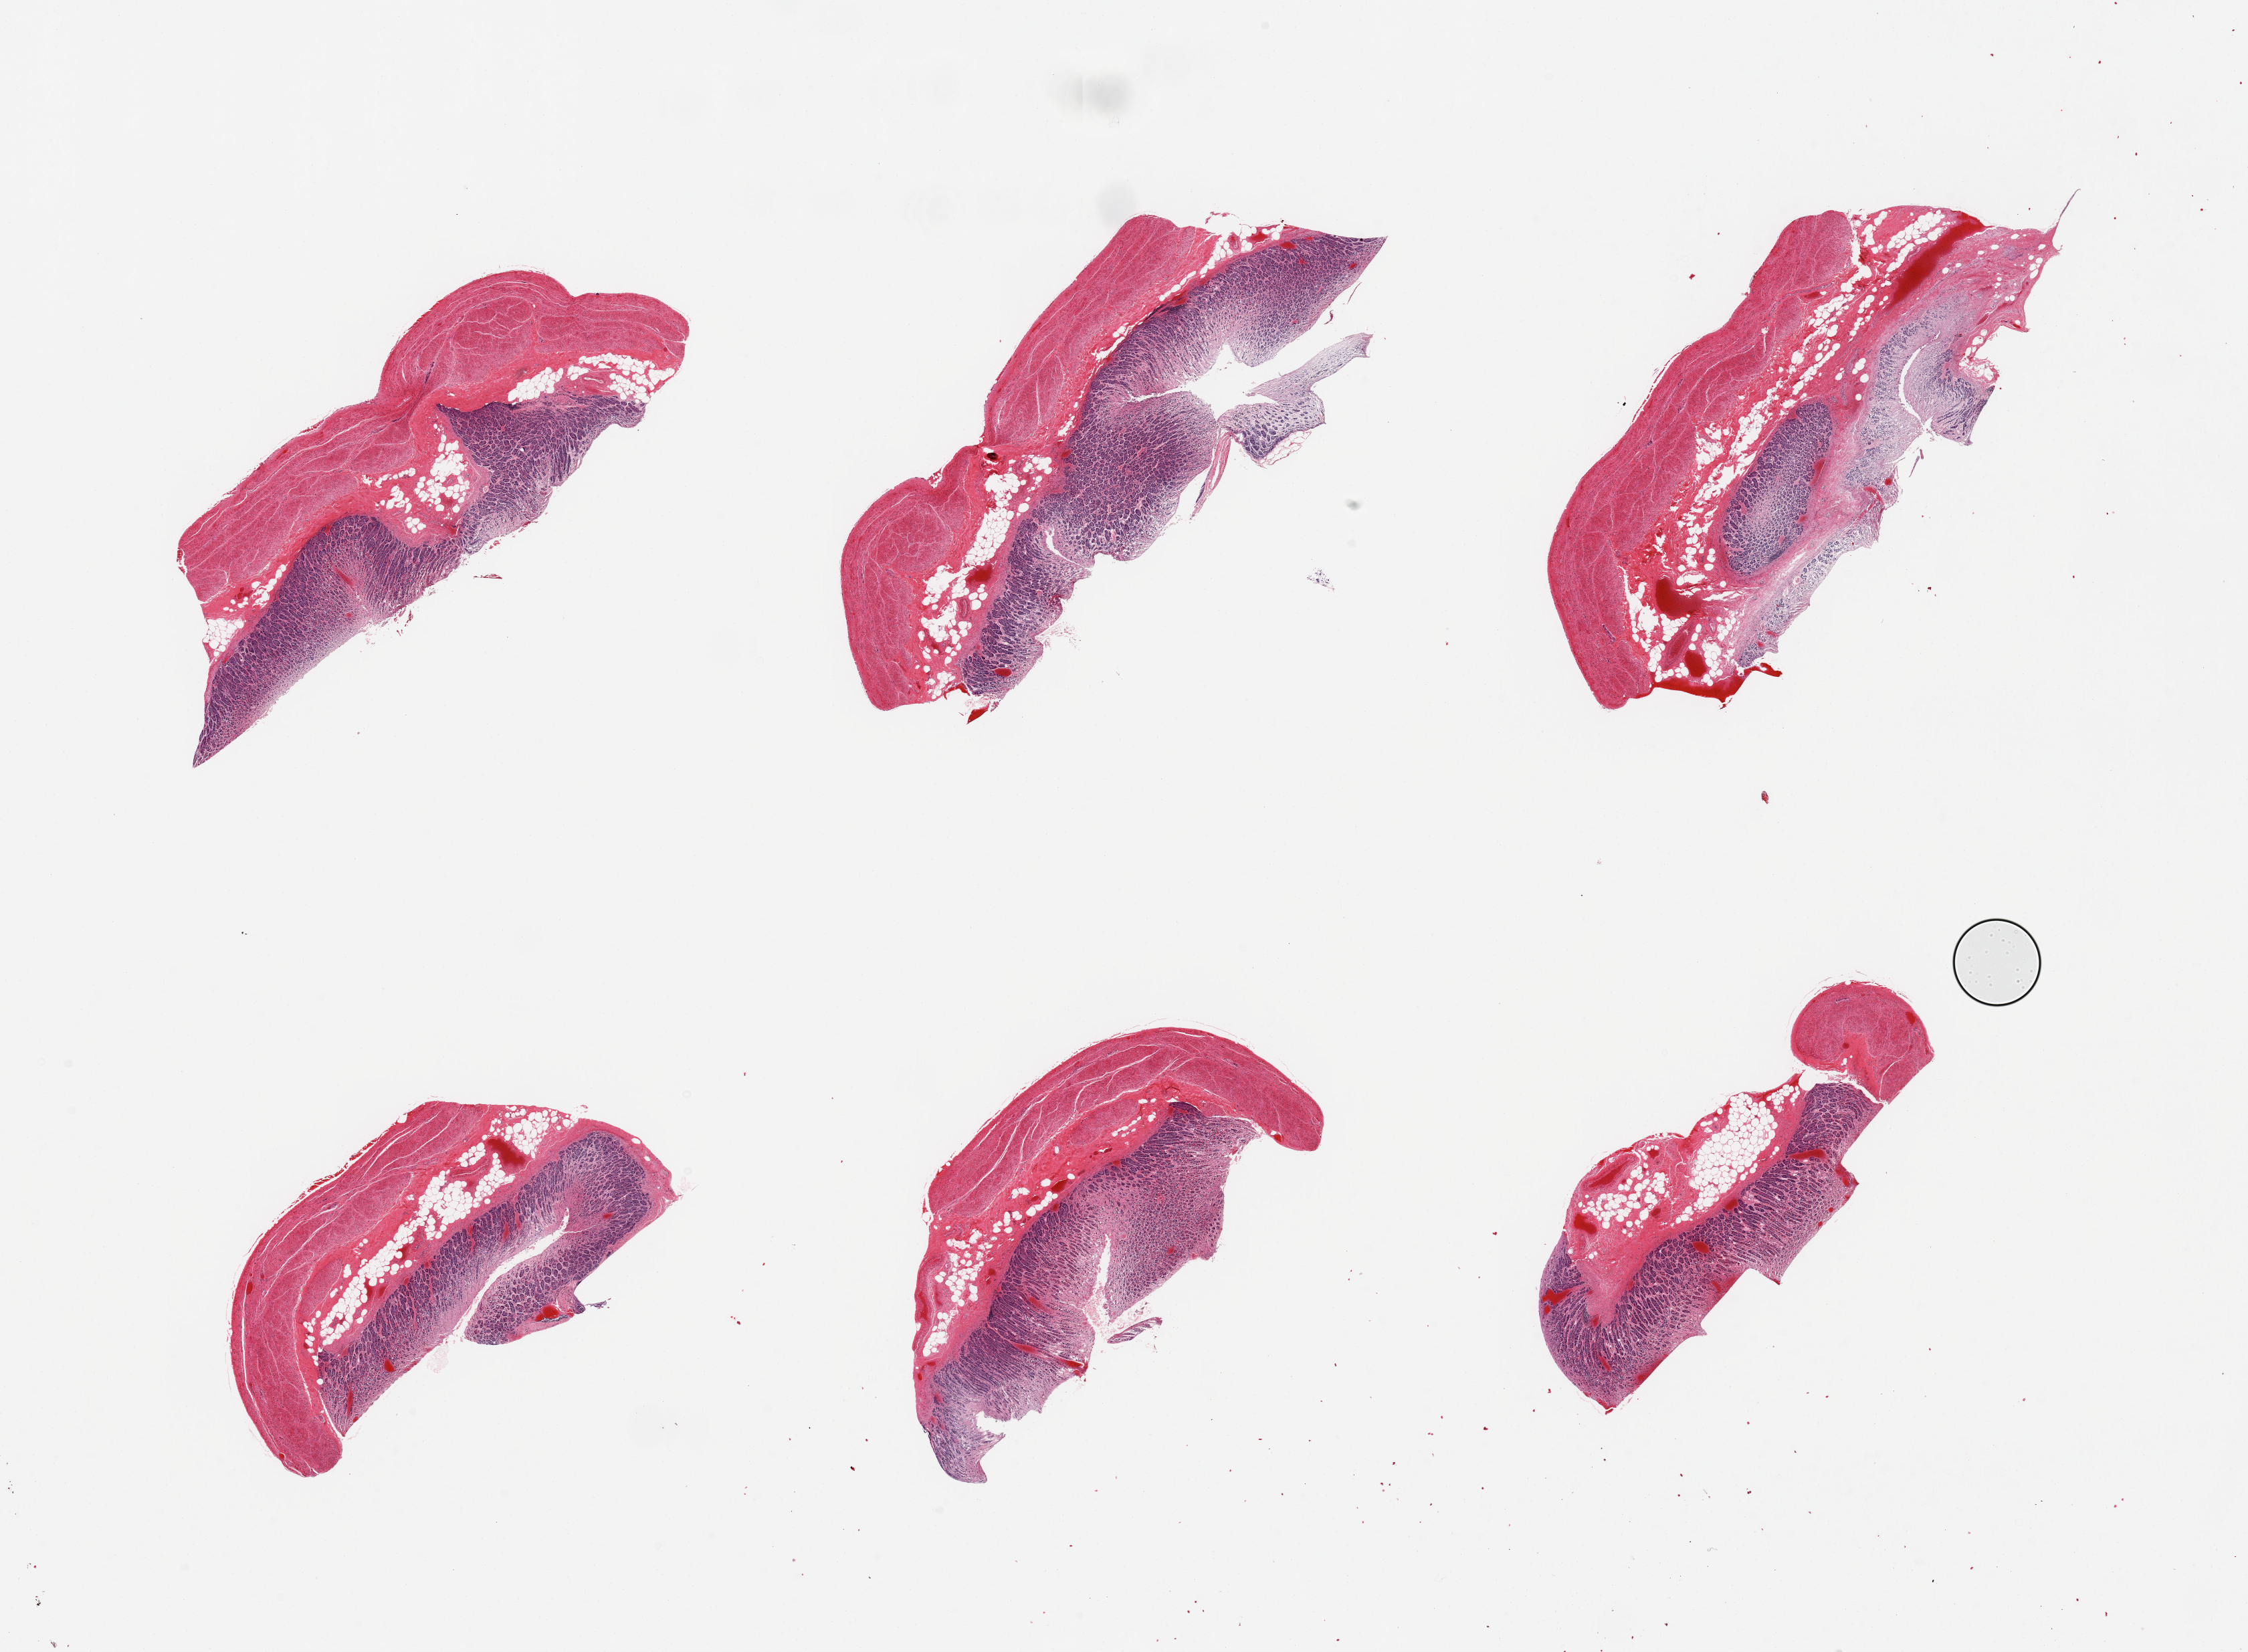
Hematoxylin and eosin (H&E) whole-slide image — whole scanned area (about 26.6 x 19.5 mm, acquisition: 20x scan) shown as a low-resolution overview; PAXgene-fixed, paraffin-embedded tissue; section of stomach (target tissue); tissue donor sample. Male donor.
Pathologist's review note for this sample: 6 pieces; superficial mucosa more autolyzed than deep; muscularis present.